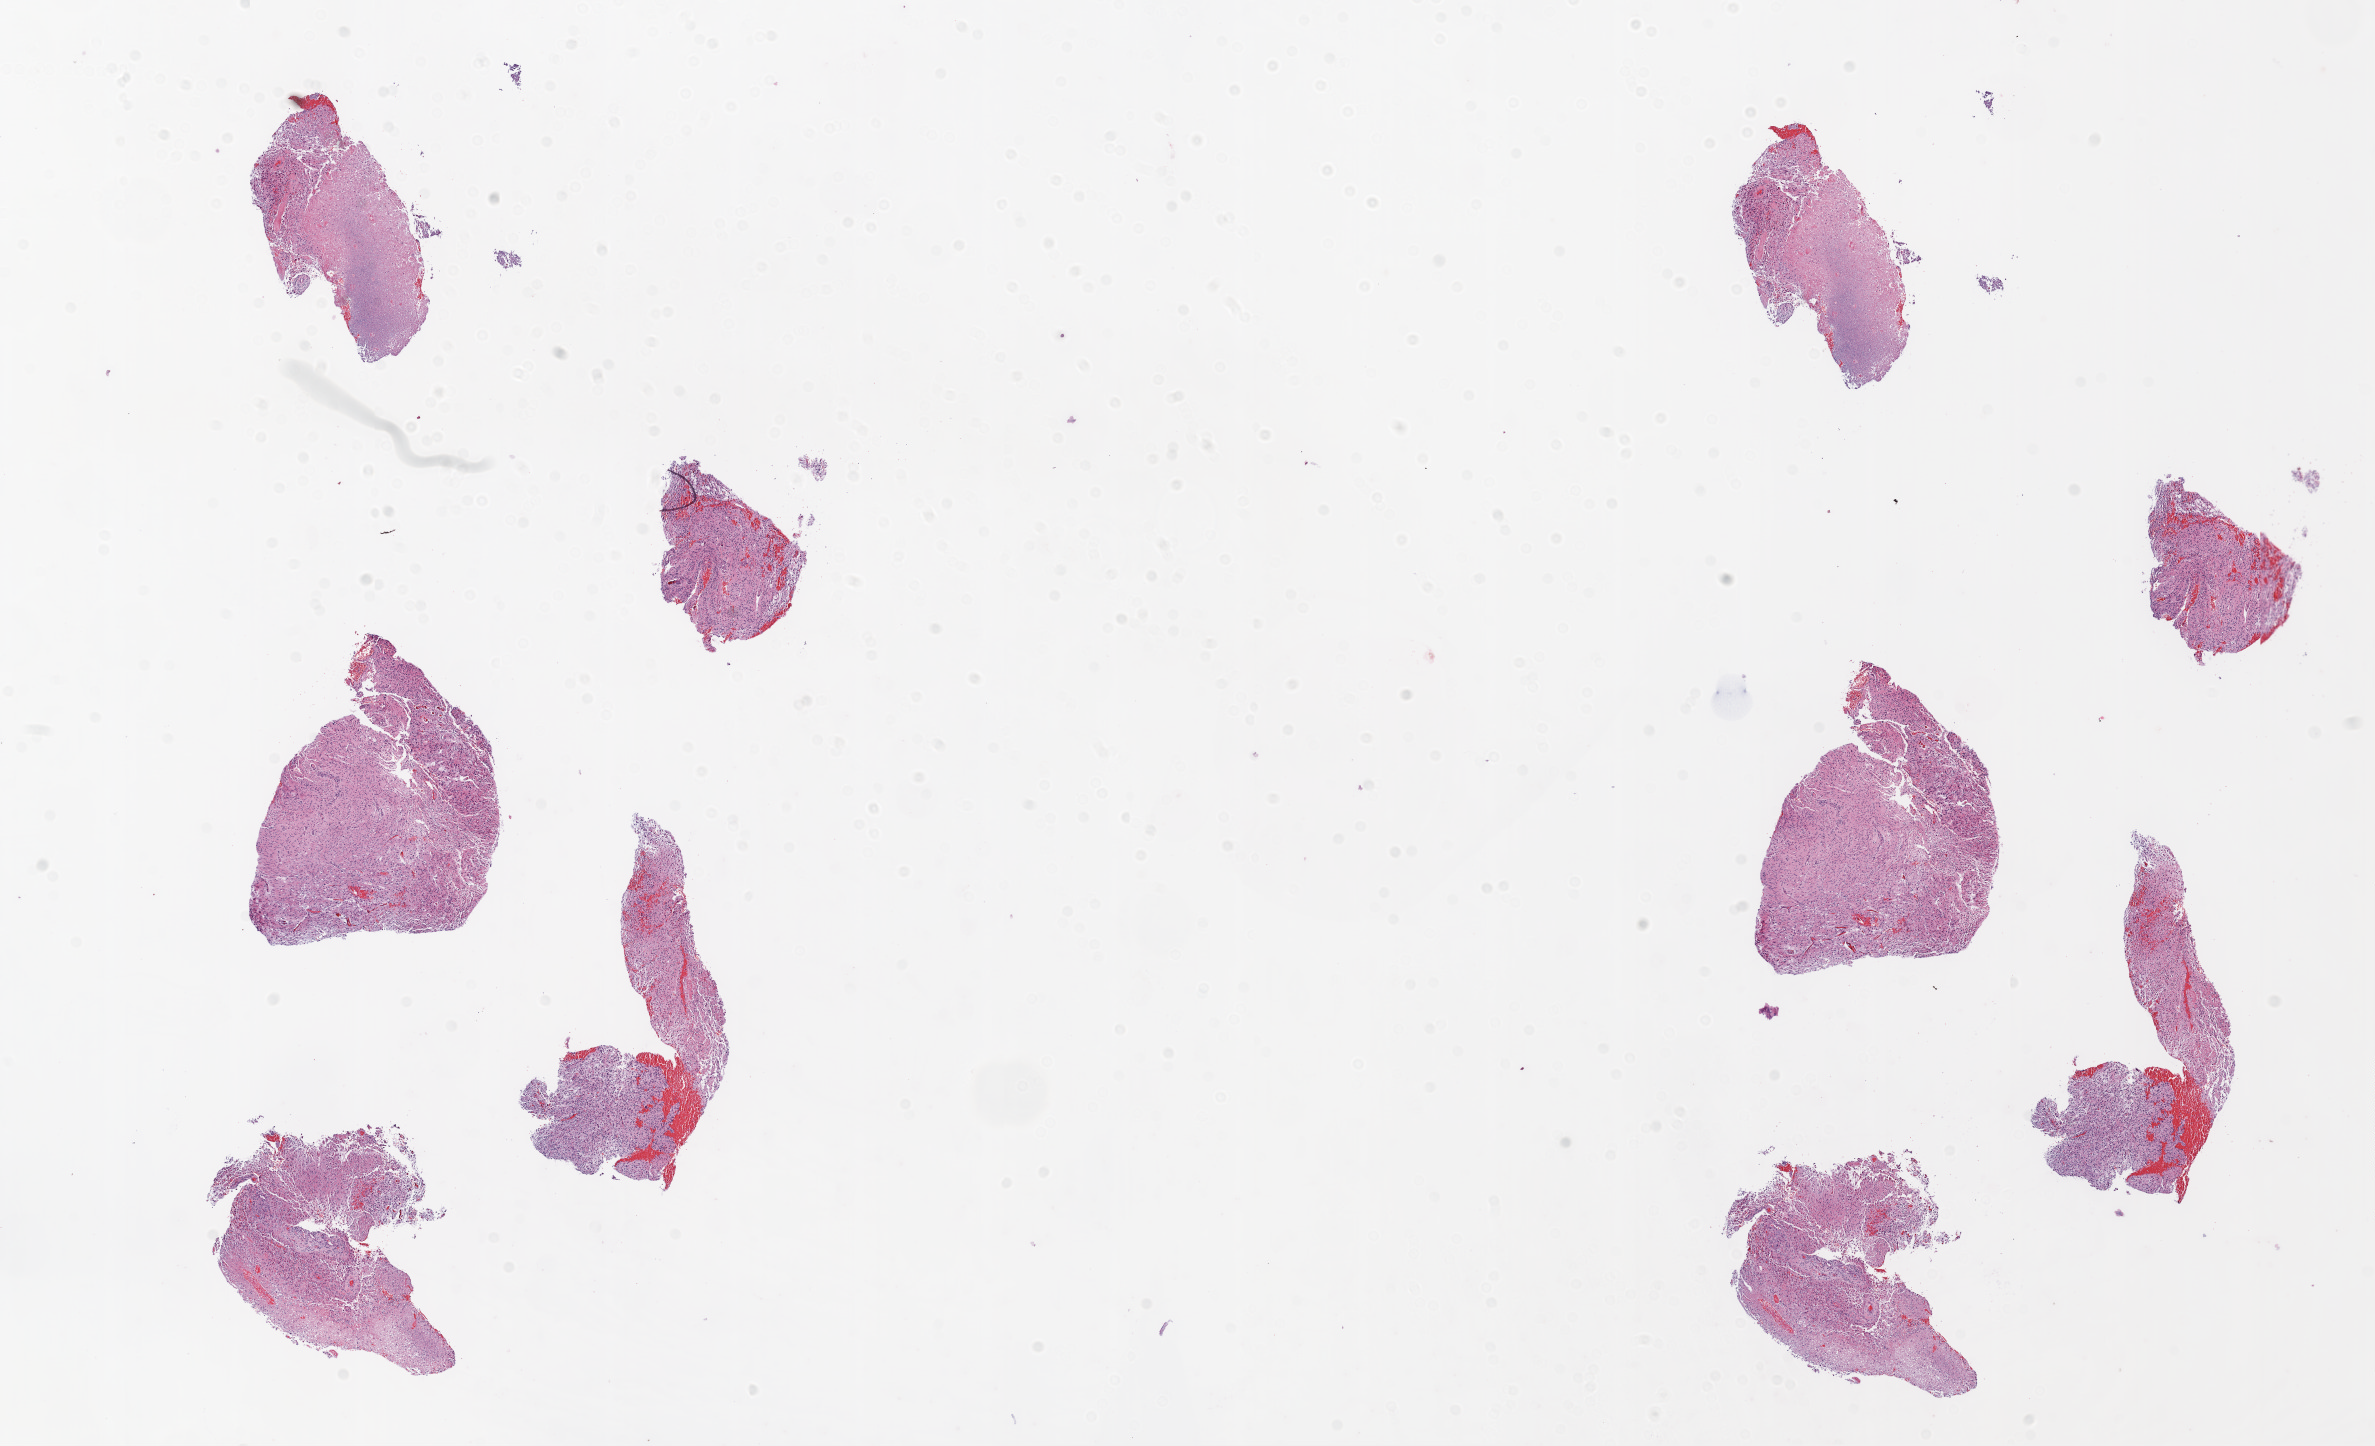
Digitized H&E-stained tissue section (whole slide) — whole scanned area (about 19.1 x 11.6 mm, from a 20x scan) shown as a low-resolution overview. Formalin-fixed paraffin-embedded (FFPE) diagnostic section. Primary tumour sample from the brain. Female patient; age at initial diagnosis 72 years.
Pathologic diagnosis: Glioblastoma.